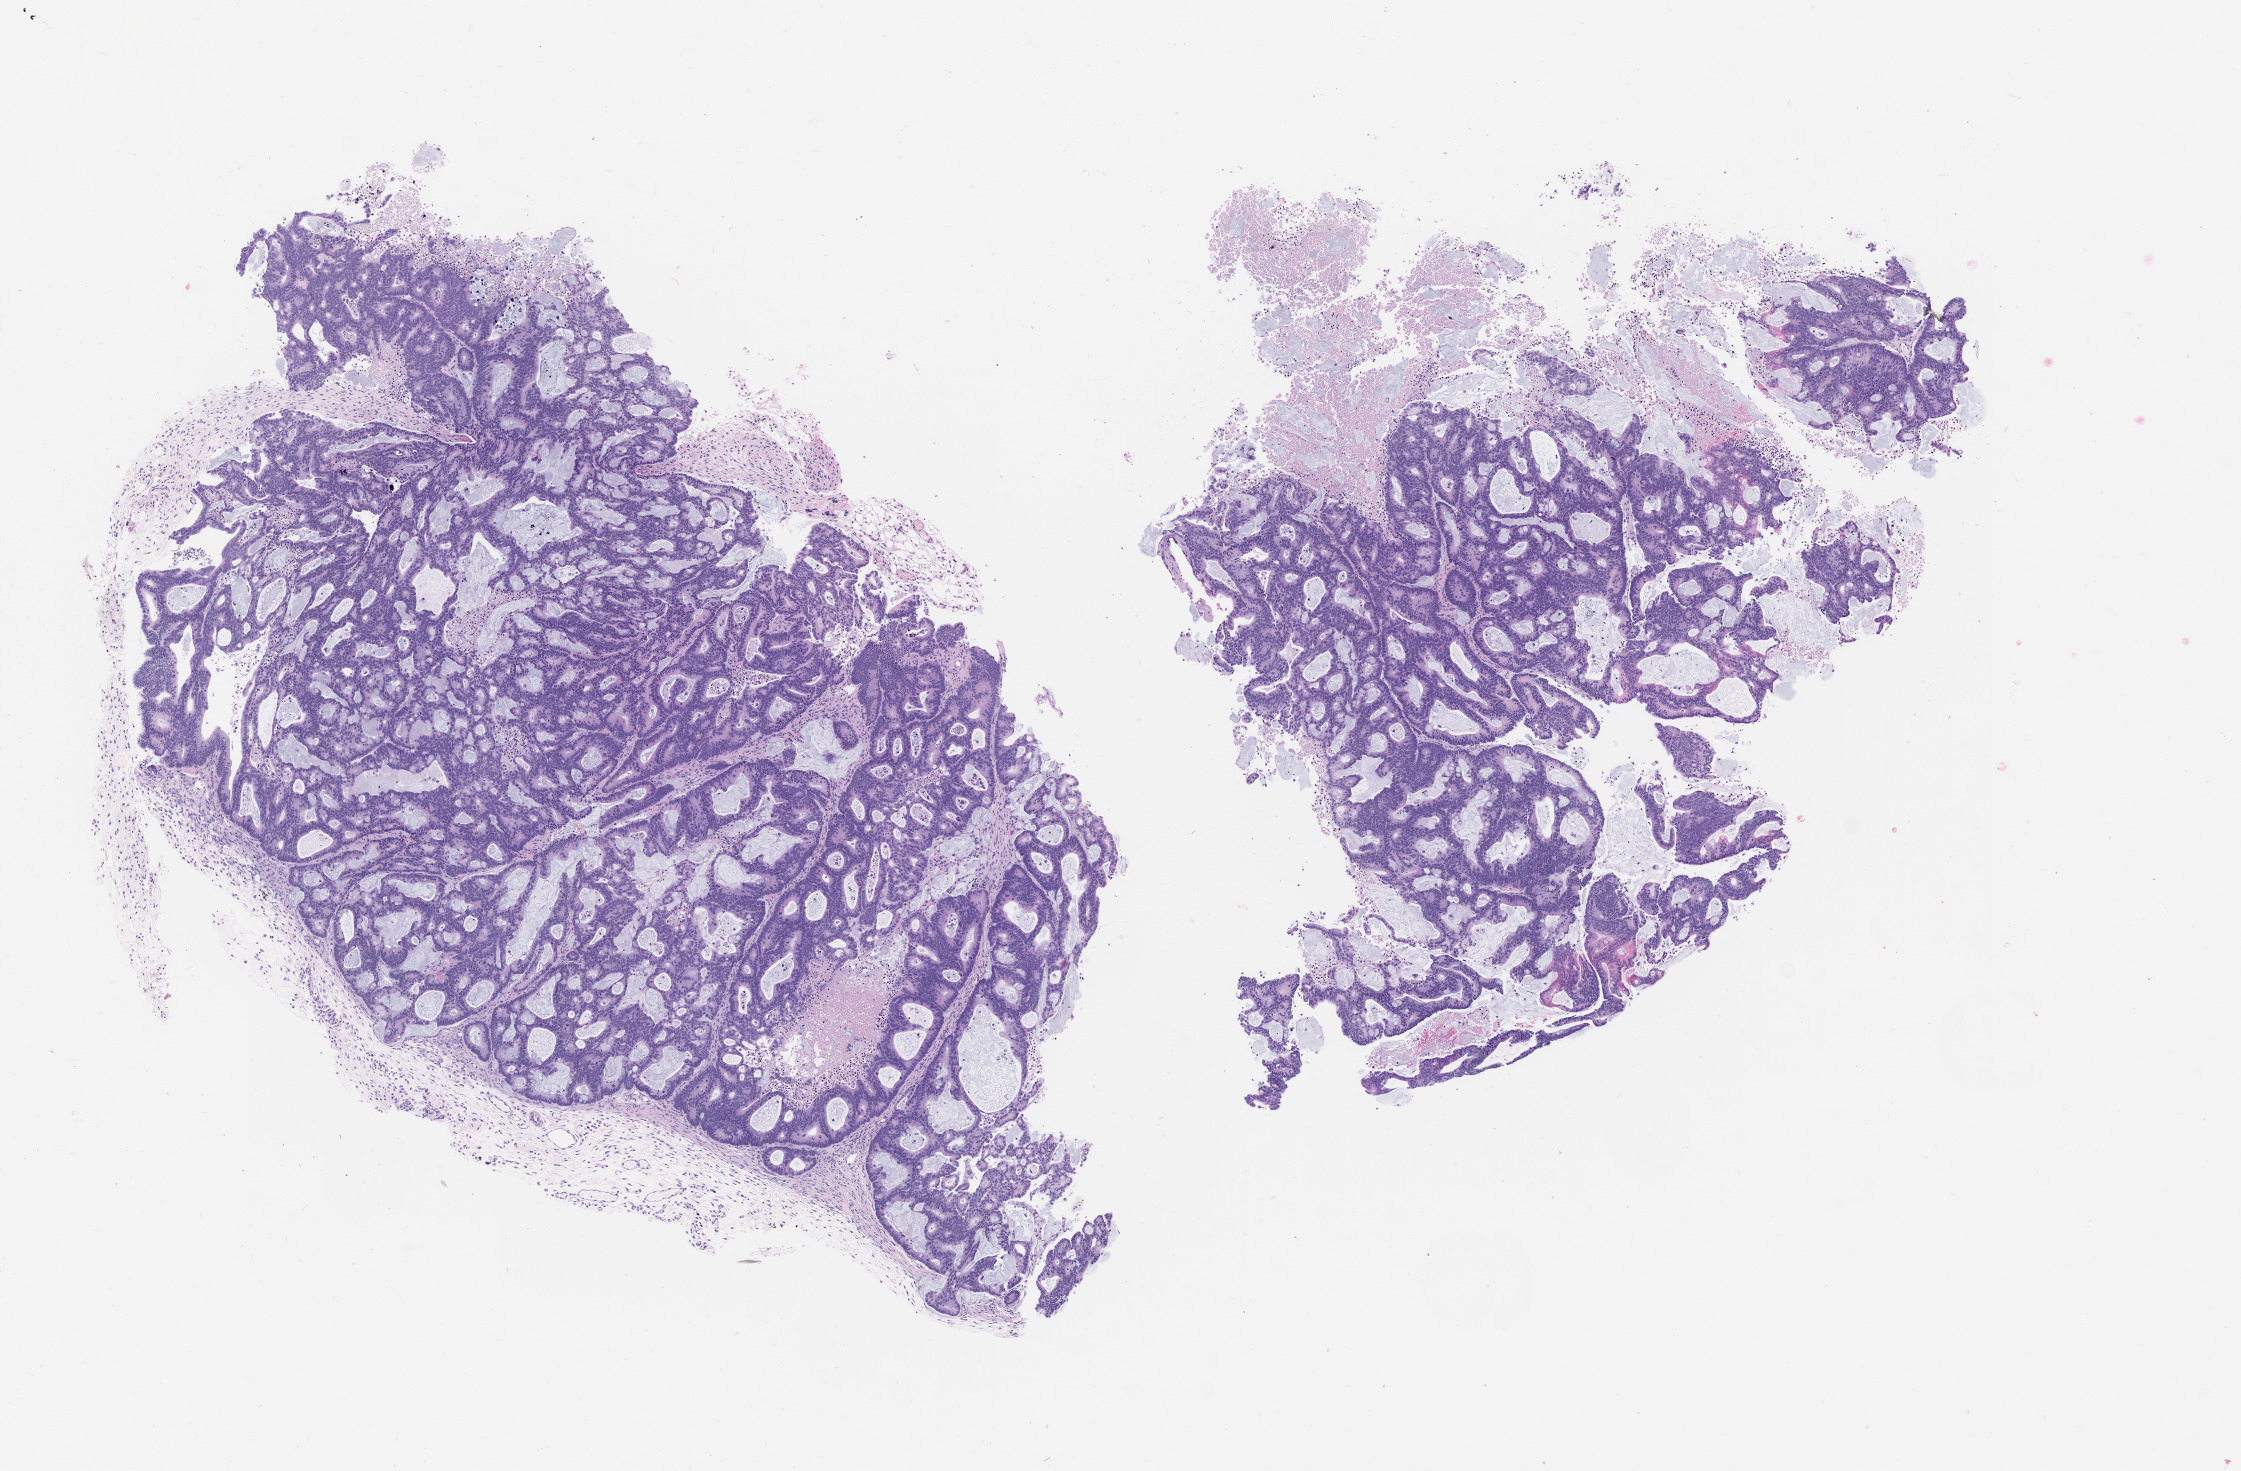
Whole-slide image, hematoxylin and eosin (H&E): patient-derived xenograft (human tumor grown in a mouse), passage 0, whole scanned area (about 9.0 x 5.9 mm) shown as a low-resolution overview; formalin-fixed paraffin-embedded section; originating tumor site category: colon.
• originating patient diagnosis: Colon Adenocarcinoma